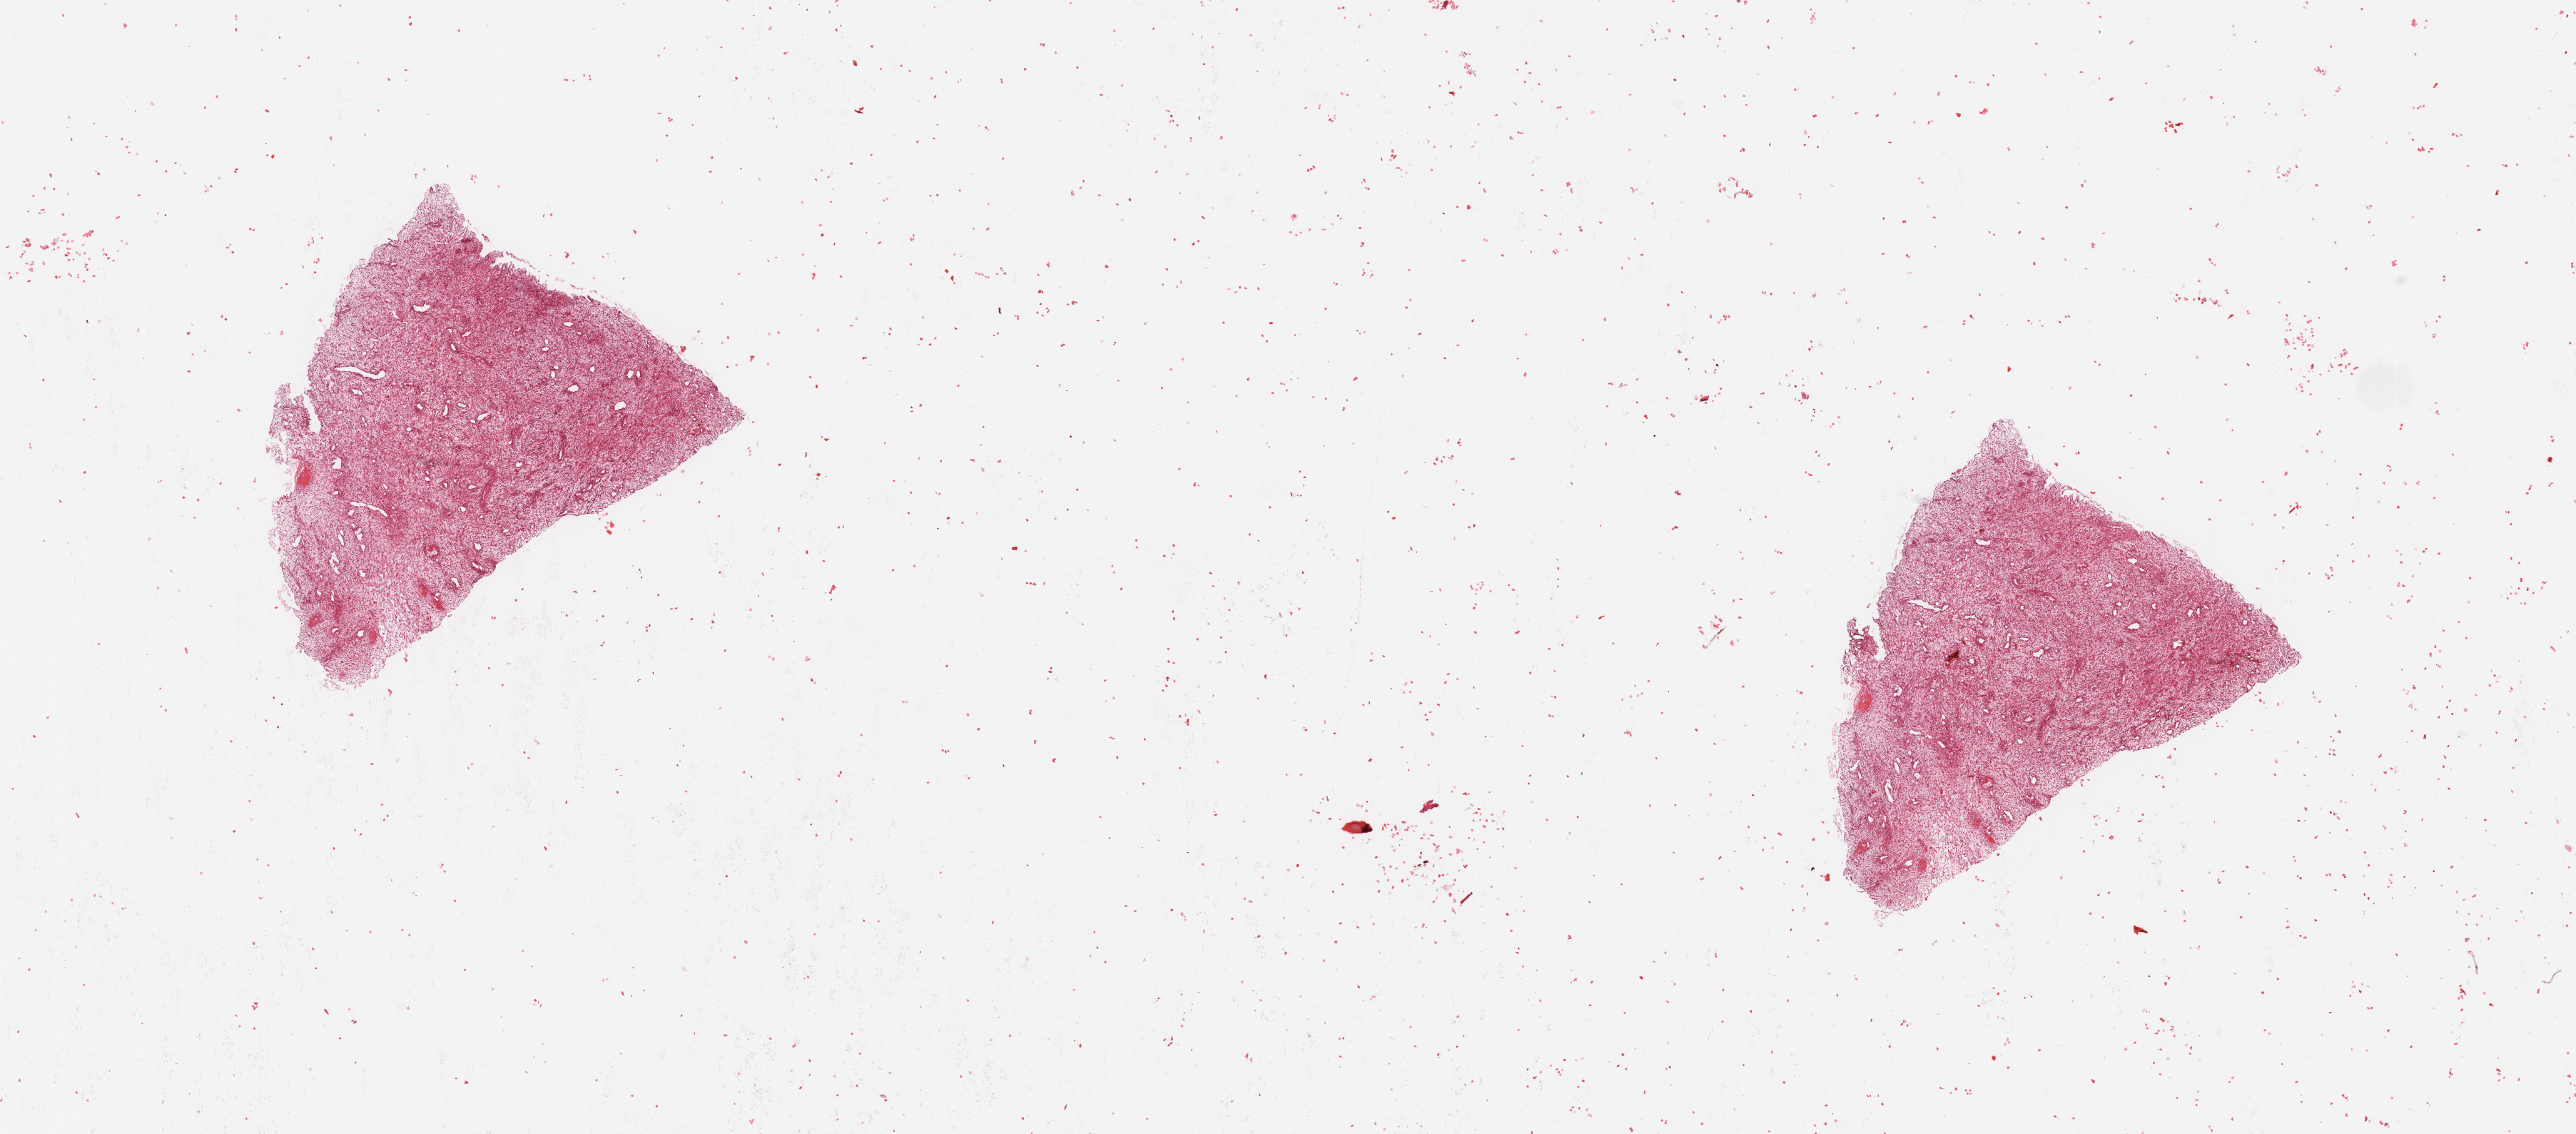
Hematoxylin and eosin (H&E) stained whole-slide image, low-resolution overview of the scanned area, about 28.5 x 12.6 mm, tumour tissue sample, sampled site: brain. Patient: male, age 59 years. Composition of this section per pathologist review: tumour nuclei 90%, necrosis 3%.
• diagnosis: Glioblastoma
• primary tumour site (as recorded): temporal lobe